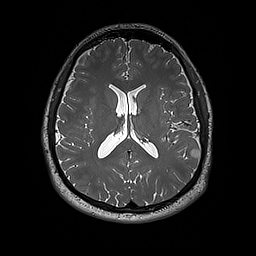
Brain MRI from a brain-tumour surgery series, one axial slice. Position 88 of 192 along the scan axis. 1 mm slice thickness. 256 × 256 image matrix. From the clinical record (not read from this slice): histopathology: Dysembryoplastic neuroepithelial tumor; WHO grade: 1; IDH mutation: no; tumour location: Left Inferior Parietal.
Annotated regions visible in this slice (manually delineated by an expert):
- tumour: bounding box <190,149,201,160> (left, top, right, bottom; pixels)